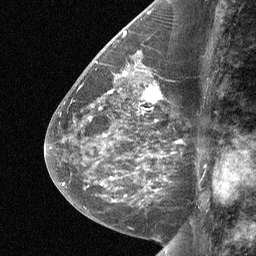
Breast MRI (dynamic contrast-enhanced), one sagittal slice. Slice 30 of 64 in the series (ordered by position). Dynamic contrast-enhanced study with each time point stored as its own series, time point 2 of 3 at this slice position (early post-contrast, ordered by acquisition time). 1.5 T. TE 4.8 ms, TR 27 ms. 2 mm slice thickness. 256 × 256 image matrix. Patient: female, 59 years. Case-level facts recorded for this patient, not image findings: setting: breast cancer imaged before/during neoadjuvant chemotherapy; receptor status: triple-negative.
Structures marked on this image (semi-automatic segmentation, software-assisted and operator-edited):
- analysis volume of interest (the breast-tissue region the enhancement analysis was run in; not a lesion): bounding box (x1, y1, x2, y2) in pixels: (126, 75, 173, 114)
- tumour enhancement mask (voxels above the 90 % enhancement threshold inside the analysis volume of interest): (142, 85, 163, 104)